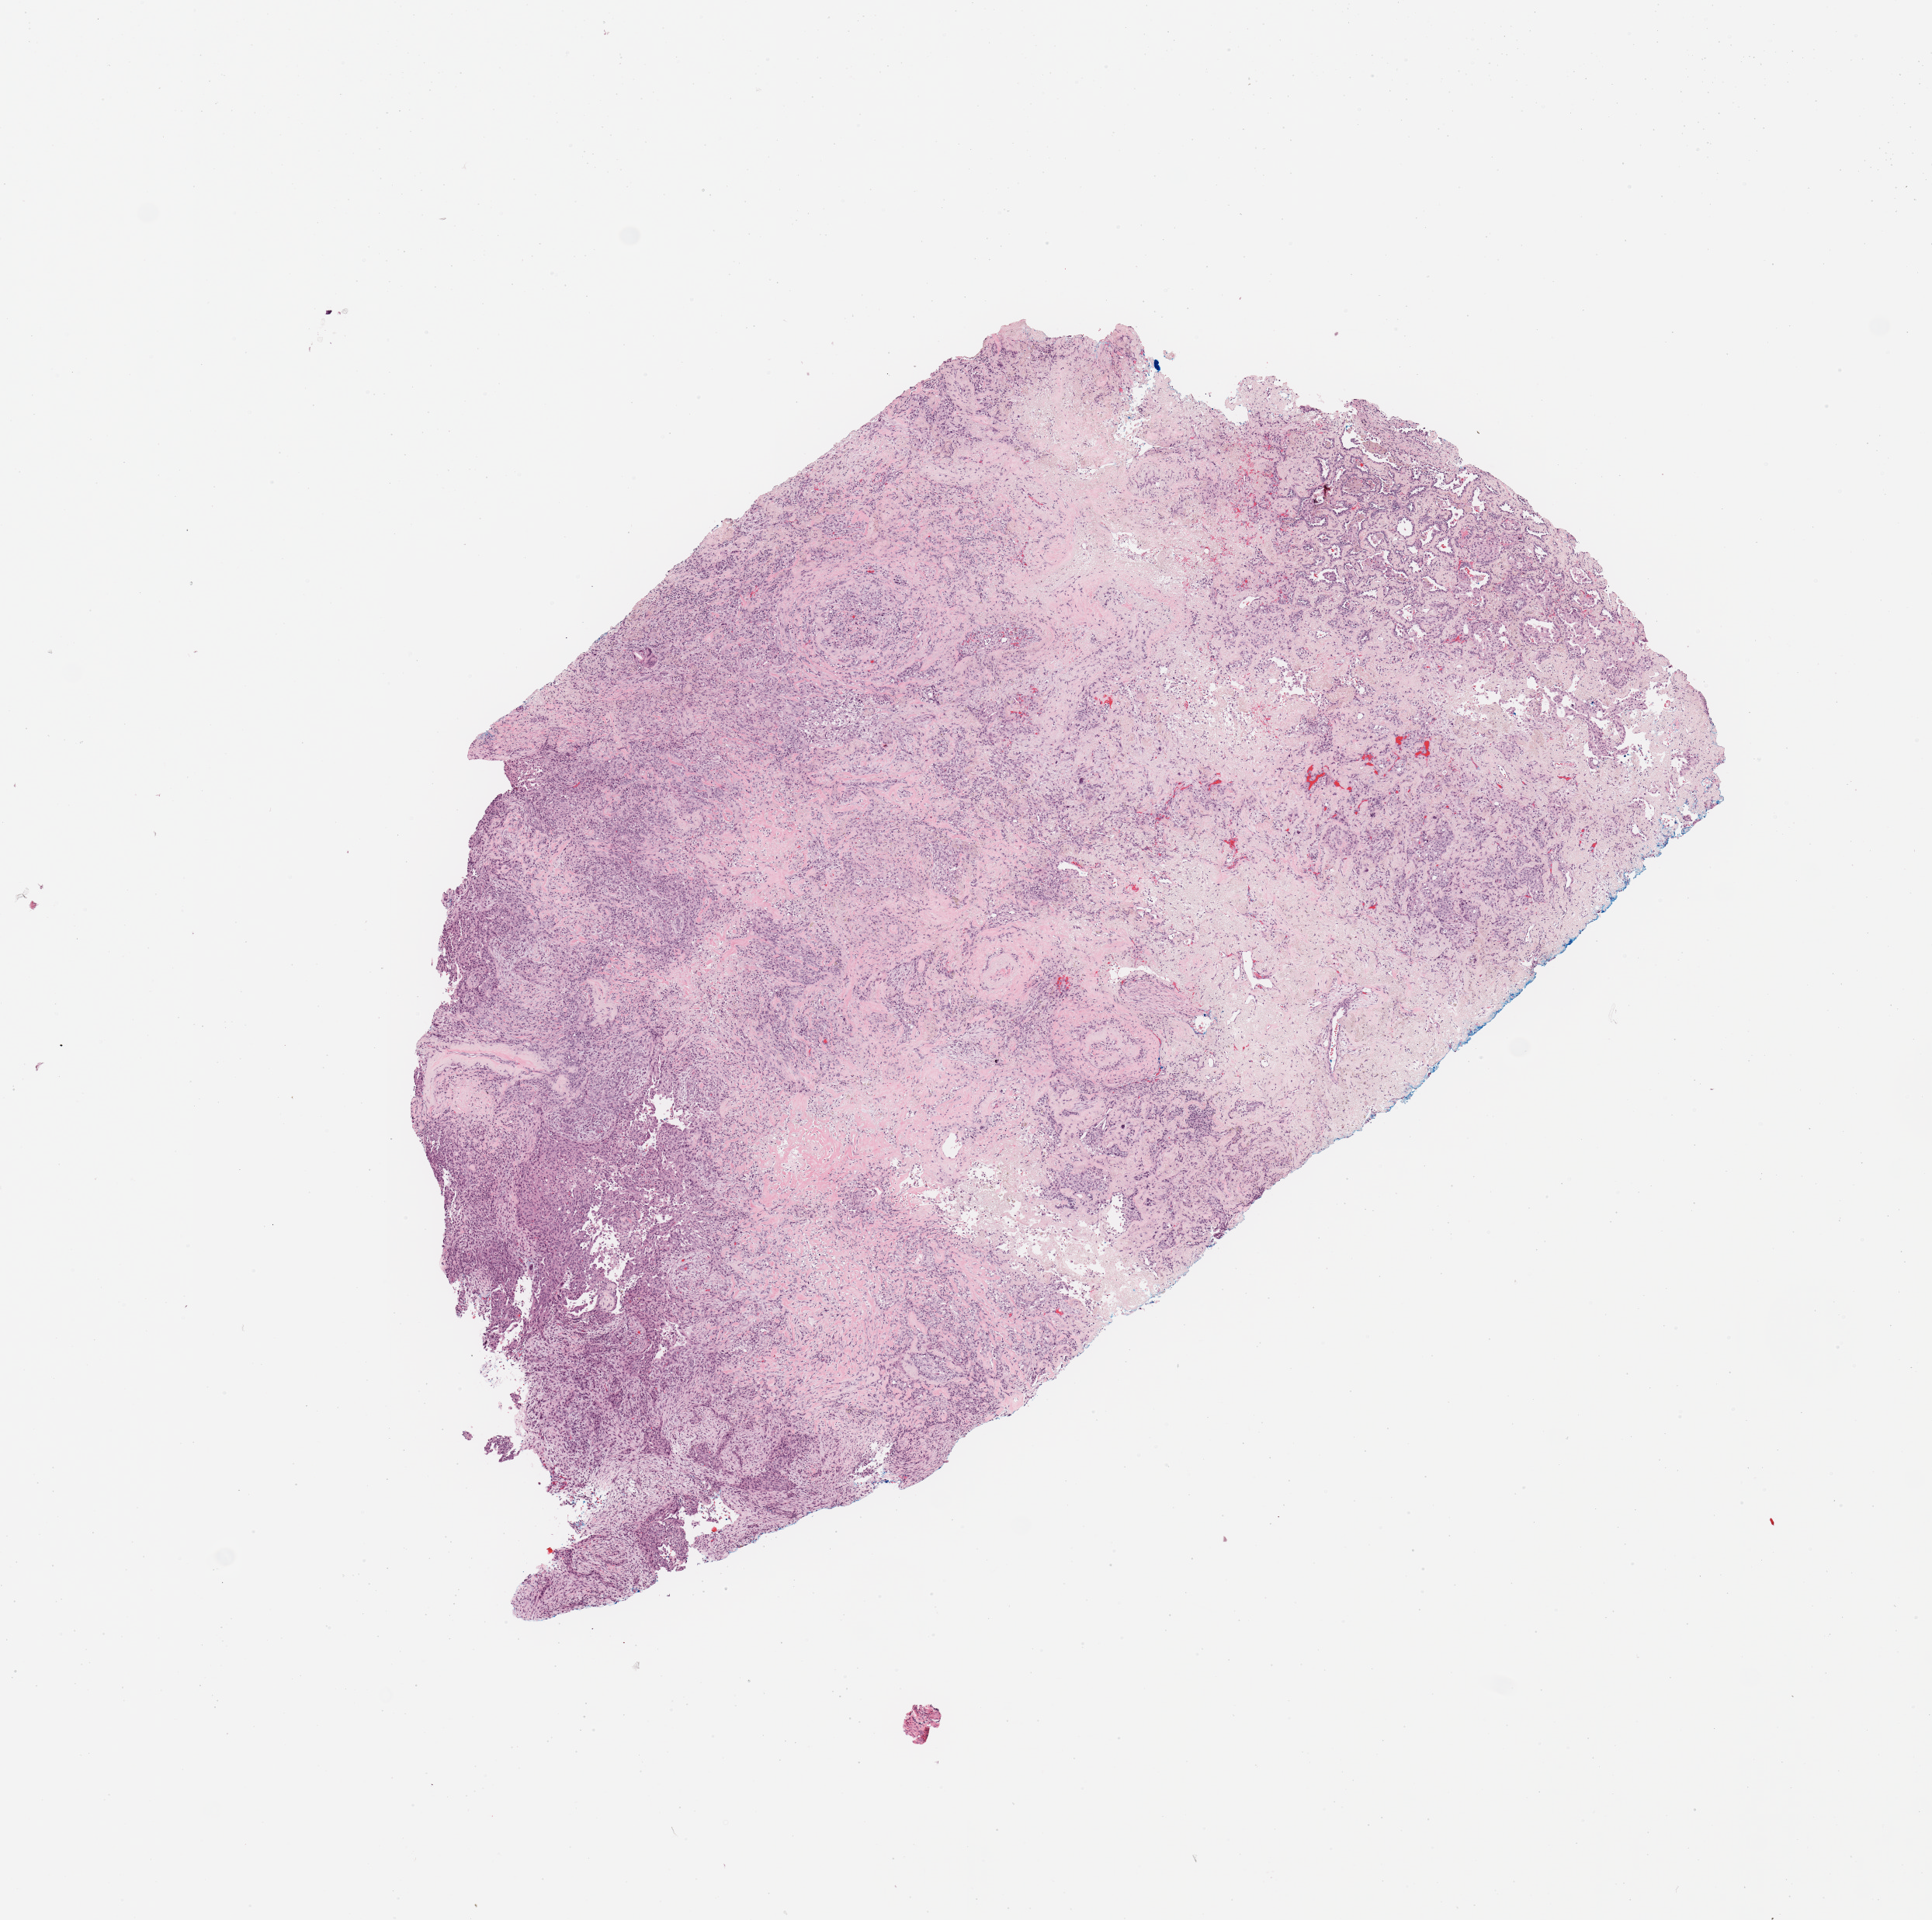
Whole-slide histology image, Hematoxylin and eosin (H&E) stained — low-resolution overview of the scanned area, about 9.8 x 9.8 mm (from a 20x scan); tumour tissue sample, sampled site: lung. Patient: male, age 71 years. Histologic grade: G2 (moderately differentiated). Composition of this section per pathologist review: tumour nuclei 70%, necrosis 0%.
• primary tumour site (as recorded): left upper lobe
• AJCC pathologic stage: IIB
• histologic diagnosis: Adenocarcinoma, NOS